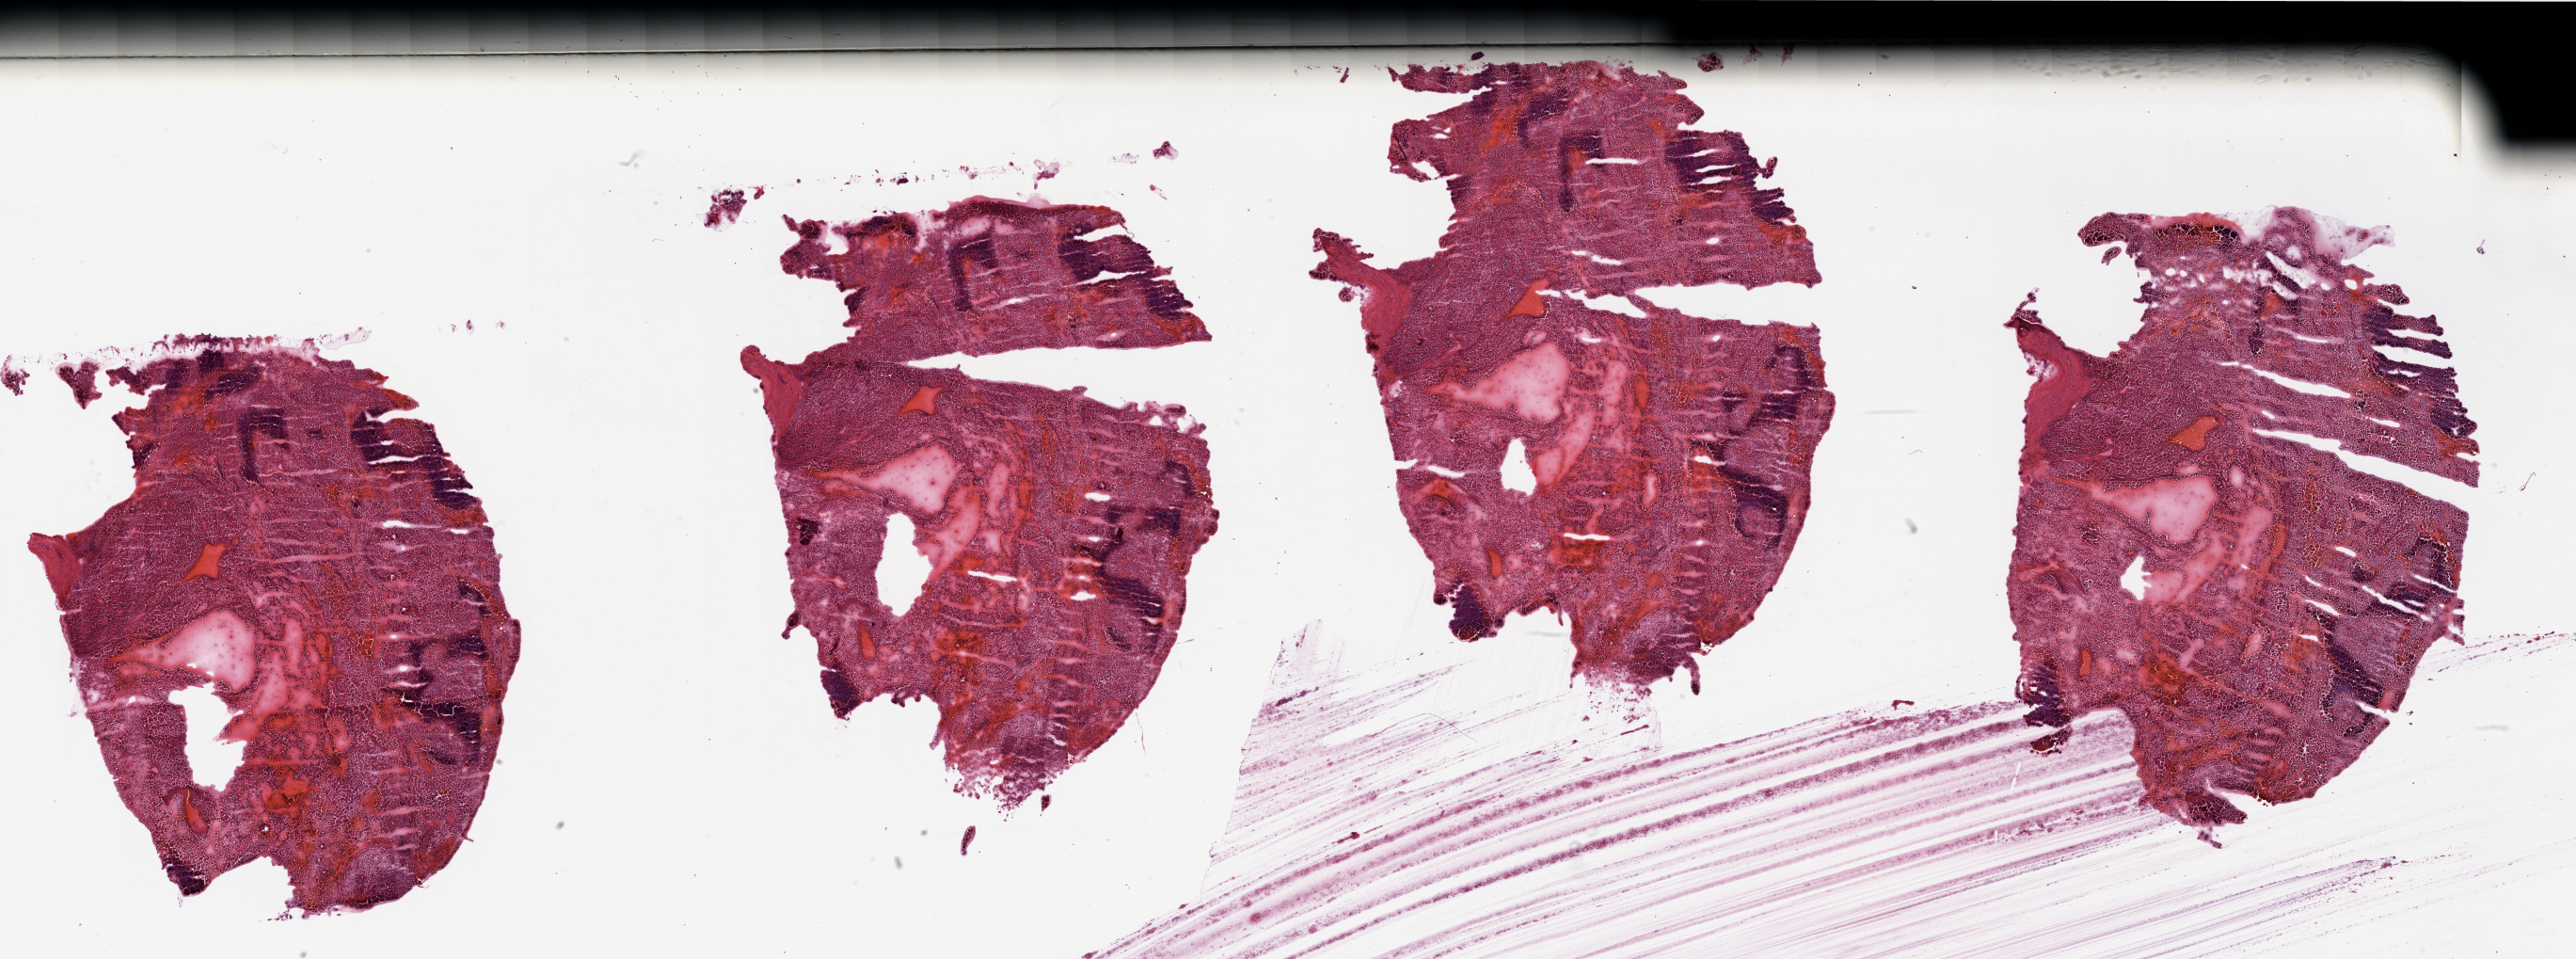
H&E-stained whole-slide image — shown as a low-resolution overview of the whole scanned area (about 43.3 x 16.1 mm, slide scanned at 20x). Tumour tissue sample, sampled site: kidney. Patient: male, age 84 years. Histologic grade: G2 (moderately differentiated). Pathologist review of this section (percent, as recorded): tumour nuclei 80%, necrosis 20%.
Diagnosis: Renal cell carcinoma, NOS. AJCC pathologic stage: III. Primary tumour site (as recorded): upper pole.